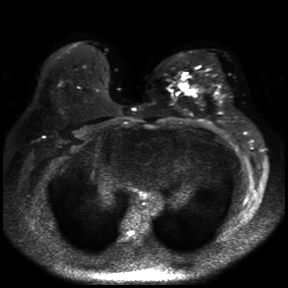
Breast MRI, one axial slice. Position 21 of 30 along the scan axis. Diffusion-weighted series; image 2 of 4 stored at this slice position (different b-values; order by instance number). 3 T. 4 mm slice thickness. 288 × 288 image matrix, field of view 360 × 360 mm. Female patient.
Outlined on this slice (outlined manually by an expert reader):
- tumour on diffusion-weighted imaging: bounding box (x1, y1, x2, y2) in pixels: (179, 83, 199, 97)